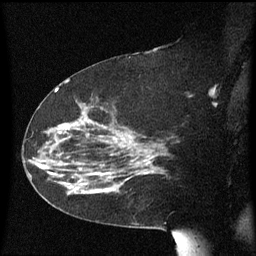
Breast MRI (dynamic contrast-enhanced), one sagittal slice. Position 33 of 60 along the scan axis. Dynamic contrast-enhanced series, image 2 of 3 at this slice position (ordered by acquisition). 1.5 T. TE 4.2 ms, TR 8.4 ms. 2.3 mm slice thickness. 256 × 256 image matrix, field of view 200 × 200 mm. Patient: female, 63 years. Case-level facts recorded for this patient, not image findings: setting: breast cancer imaged before/during neoadjuvant chemotherapy; receptor status: HER2-positive.
Structures marked on this image (semi-automatically segmented with operator editing):
- analysis volume of interest (the breast-tissue region the enhancement analysis was run in; not a lesion): box from (x=71, y=144) to (x=147, y=195) px
- tumour enhancement mask (voxels above the 70 % enhancement threshold inside the analysis volume of interest): (x=96, y=160)–(x=147, y=175)